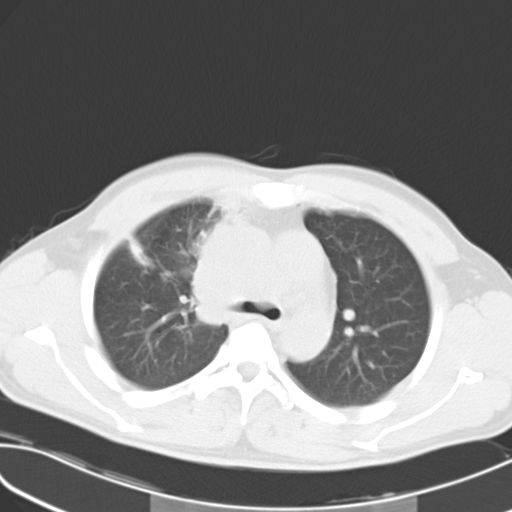
Chest CT, one axial slice. Slice 19 of 27 in the series (ordered by position). Reconstruction kernel B40f. 120 kVp. Lung window (W 1500 / L -600 HU). 10 mm slice thickness. 512 × 512 image matrix. Male patient, age 32 years. Case-level facts recorded for this patient, not image findings: clinical TNM (as recorded): T4 N3 M0; histopathological grade: G3.
Structures marked on this image (rectangle marked by the reading radiologist):
- lung tumour (recorded histology: small cell carcinoma): box from (x=180, y=215) to (x=233, y=334) px